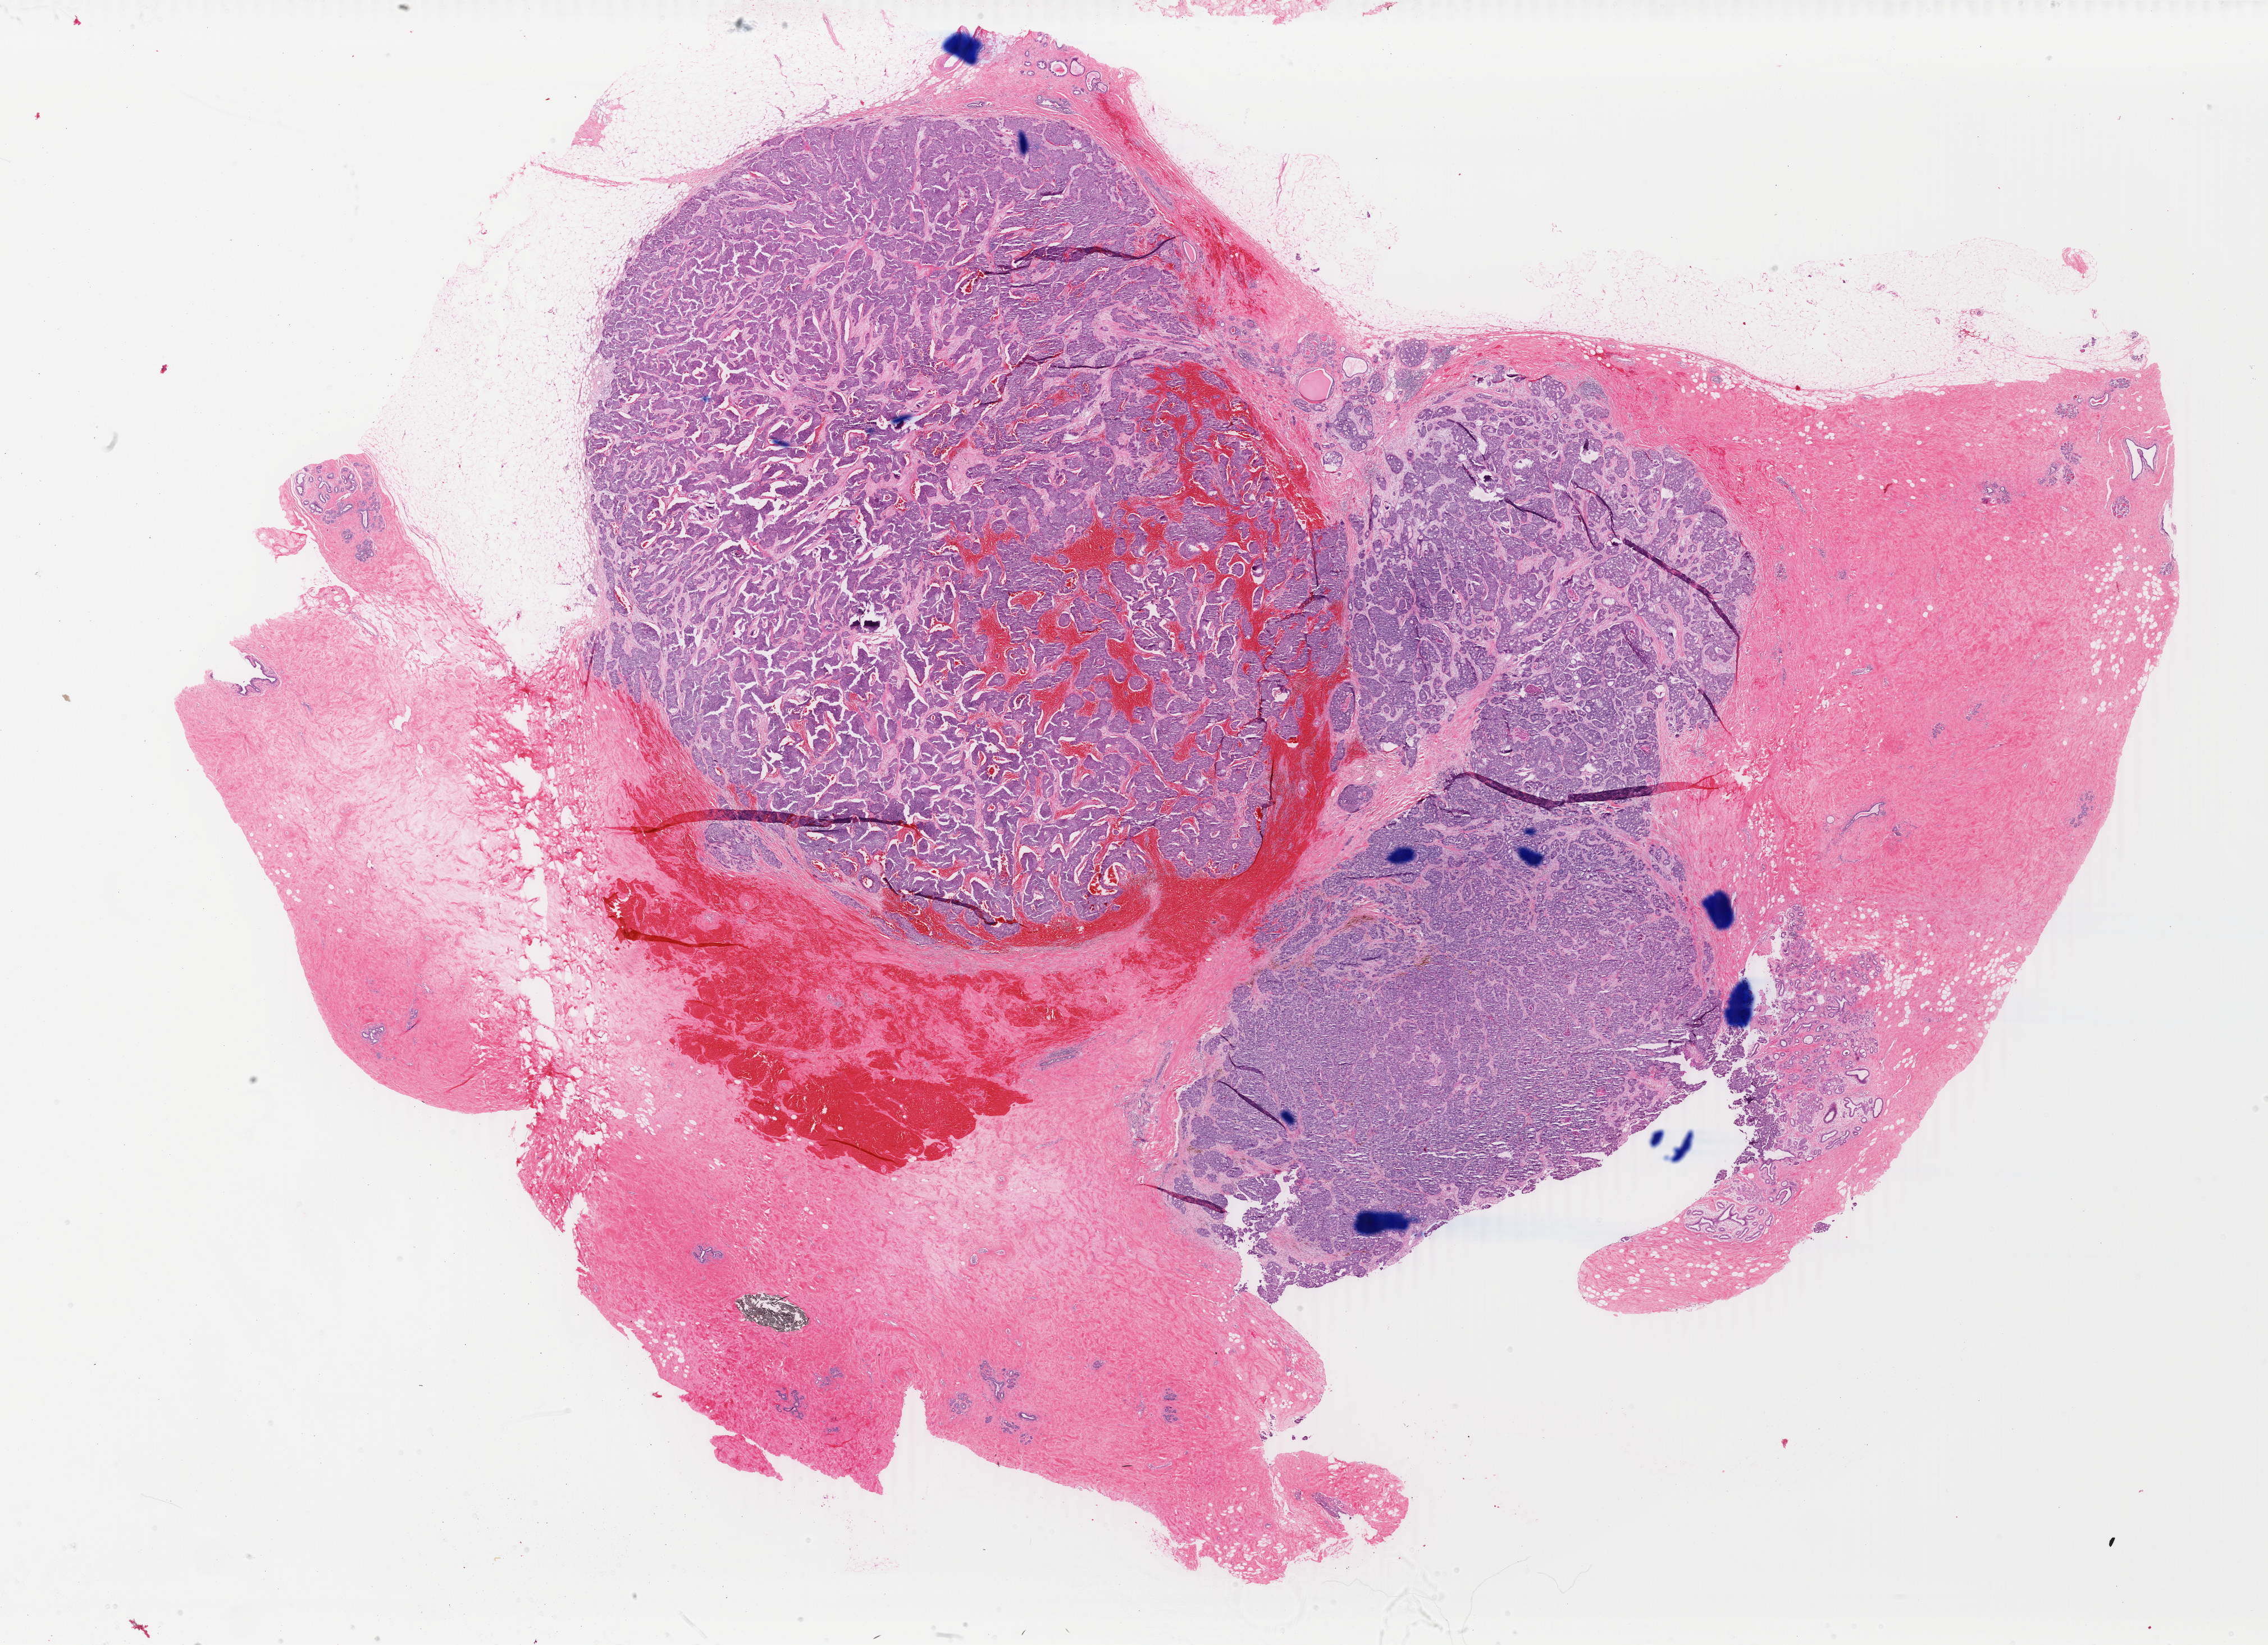
Whole-slide histology image, Hematoxylin and eosin (H&E) stained, low-resolution overview of the scanned area, about 32.1 x 23.3 mm (slide scanned at 40x), FFPE section, breast, primary tumour sample. Female, age 51 years at initial diagnosis.
Lymph nodes positive (case pathology): 0 of 15 examined. AJCC pathologic stage: IIA. Diagnosis: Infiltrating duct mixed with other types of carcinoma.